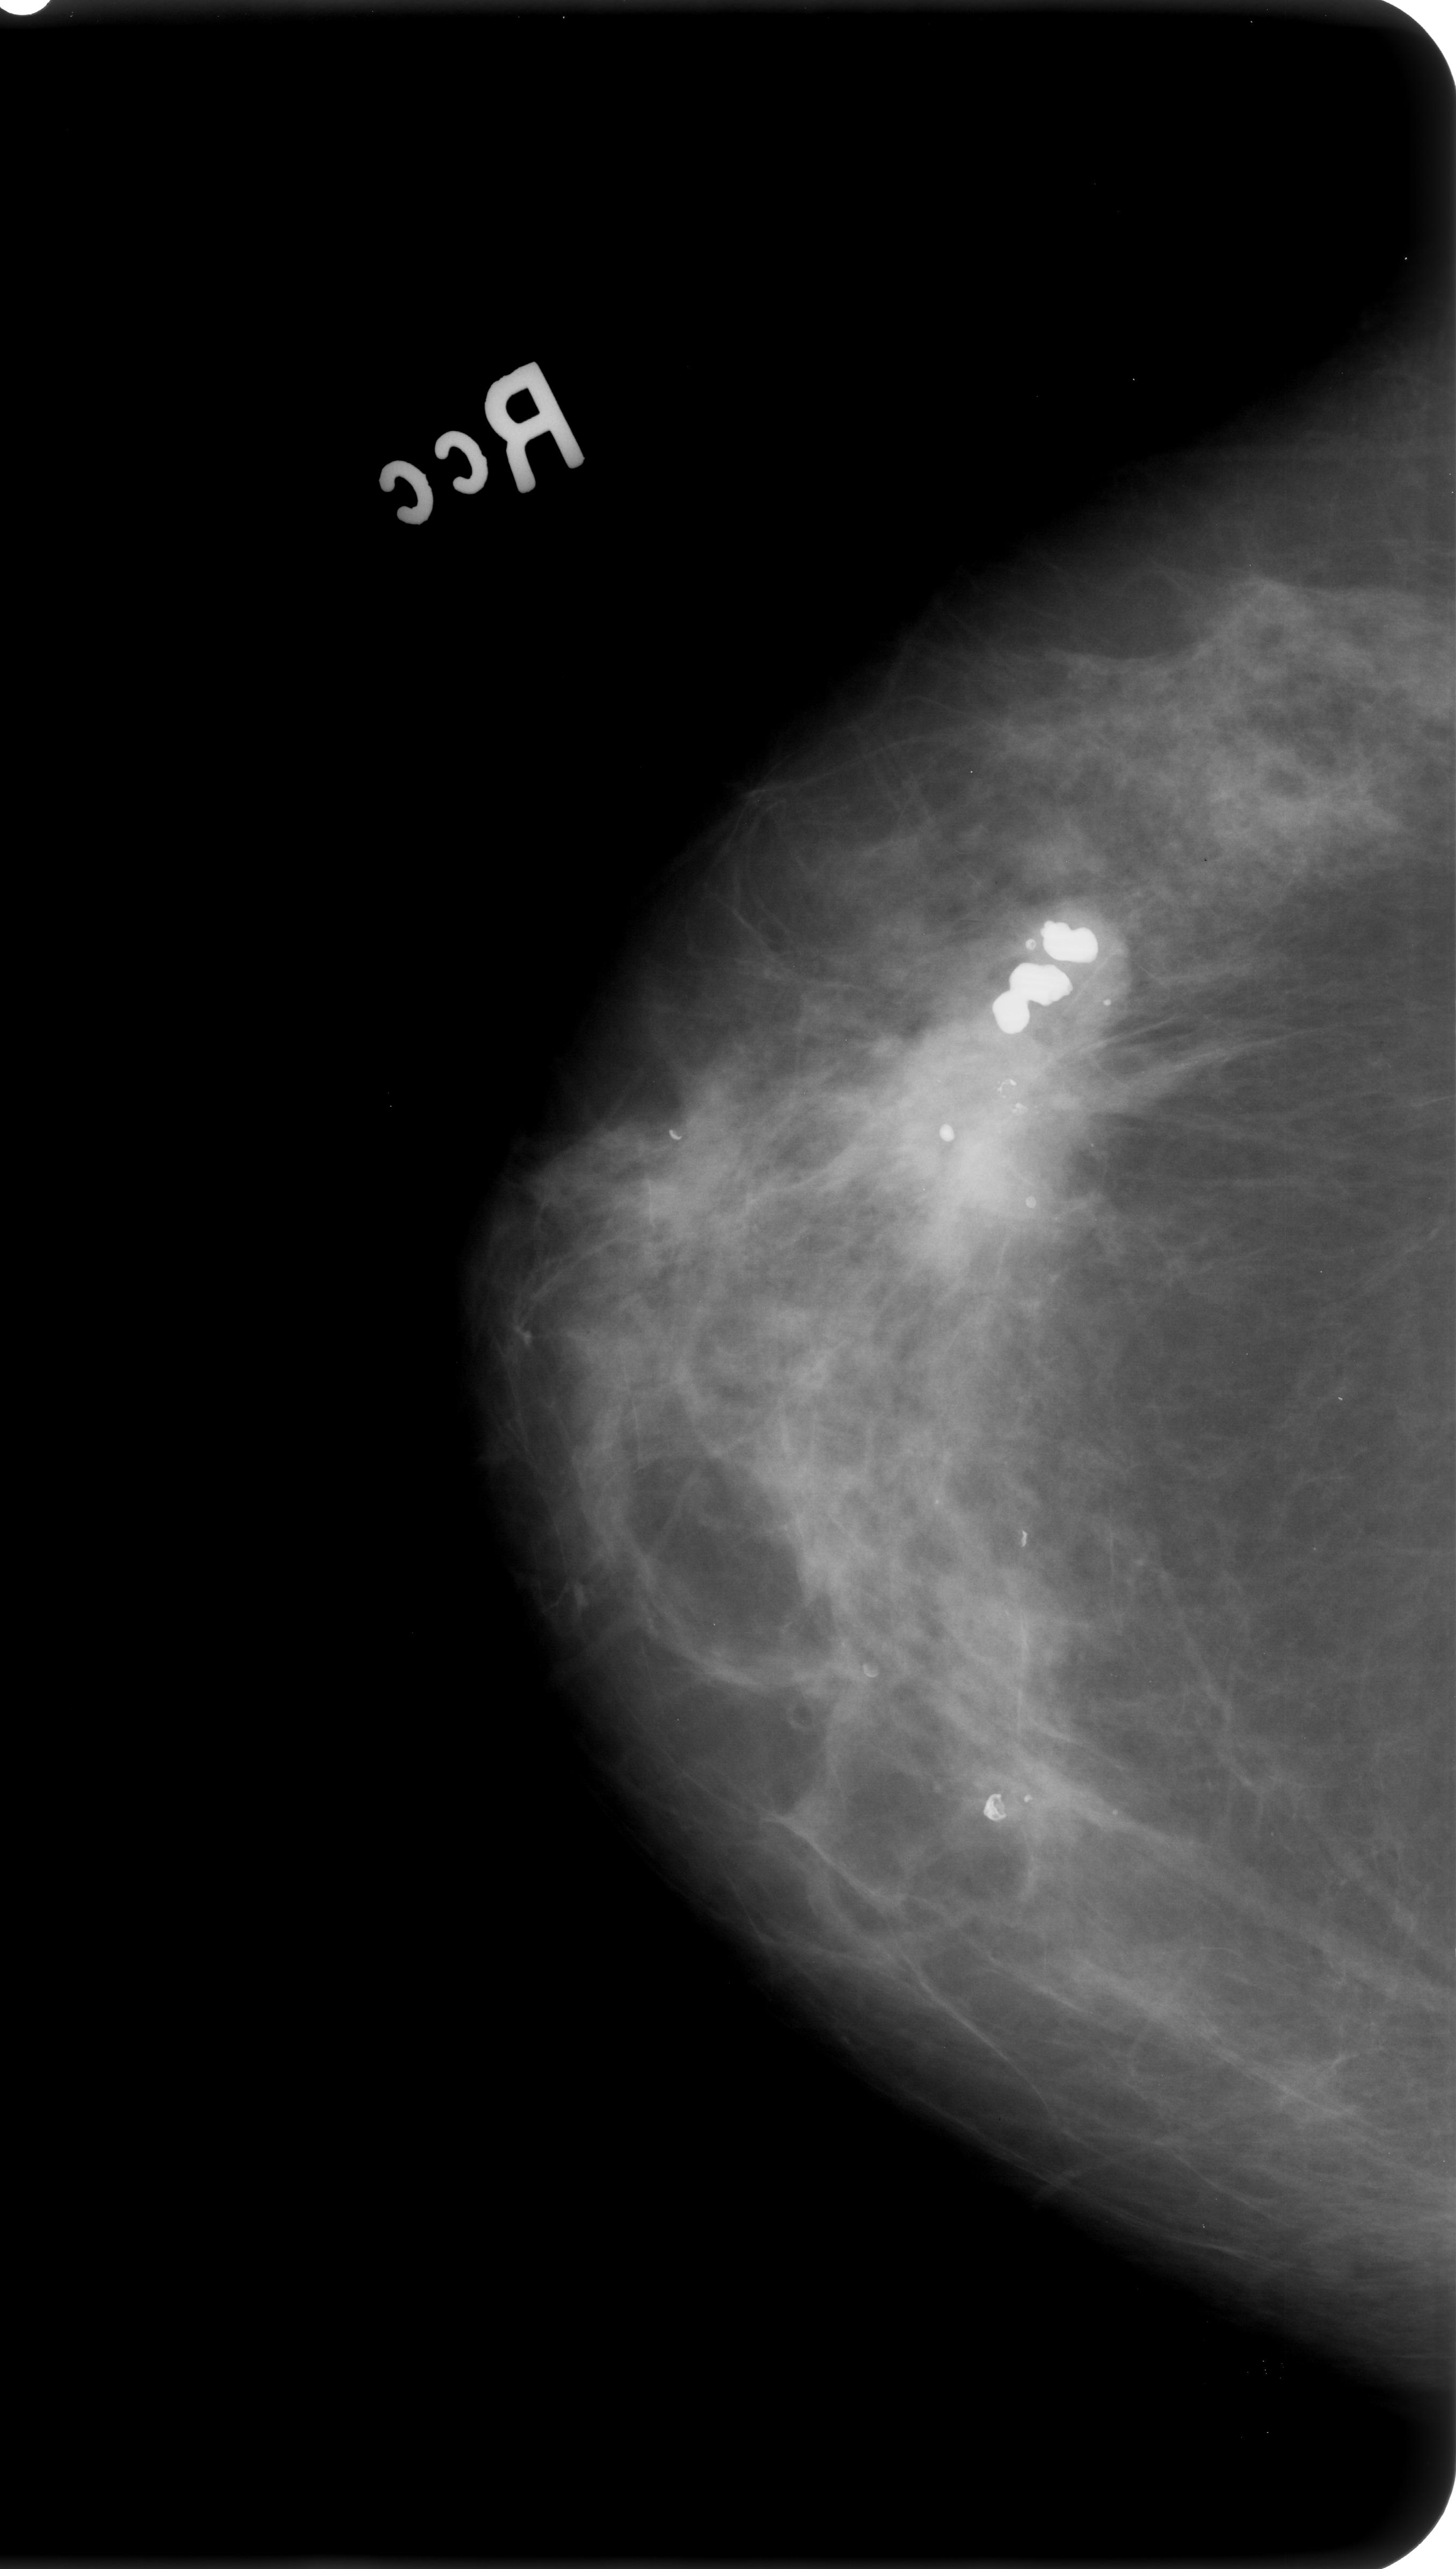
Digitized screen-film mammogram. Right breast. CC view. Breast composition: heterogeneously dense (BI-RADS density category 3 of 4). 1456 × 2569 image matrix.
Marked abnormalities (boxes around the expert regions of interest):
- Finding 1 of 2: calcifications, morphology pleomorphic, distribution clustered; BI-RADS assessment category 4; pathology result (as recorded, not read from the image): malignant: bounding box <996,1078,1032,1101> (left, top, right, bottom; pixels)
- Finding 2 of 2: calcifications, morphology pleomorphic, distribution clustered; BI-RADS assessment category 4; subtlety rating 4 on a 1 (subtle) to 5 (obvious) scale; pathology (as recorded): malignant: <1009,1099,1049,1131>